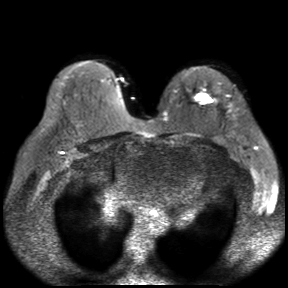
Breast MRI, one axial slice; position 16 of 30 along the scan axis; diffusion-weighted series; image 2 of 4 stored at this slice position (different b-values; order by instance number); 3 T; 4 mm slice thickness; 288 × 288 image matrix. Female patient.
Annotated regions visible in this slice (outlined manually by an expert reader):
- tumour on diffusion-weighted imaging: bounding box [x1, y1, x2, y2] px = [201, 96, 209, 102]